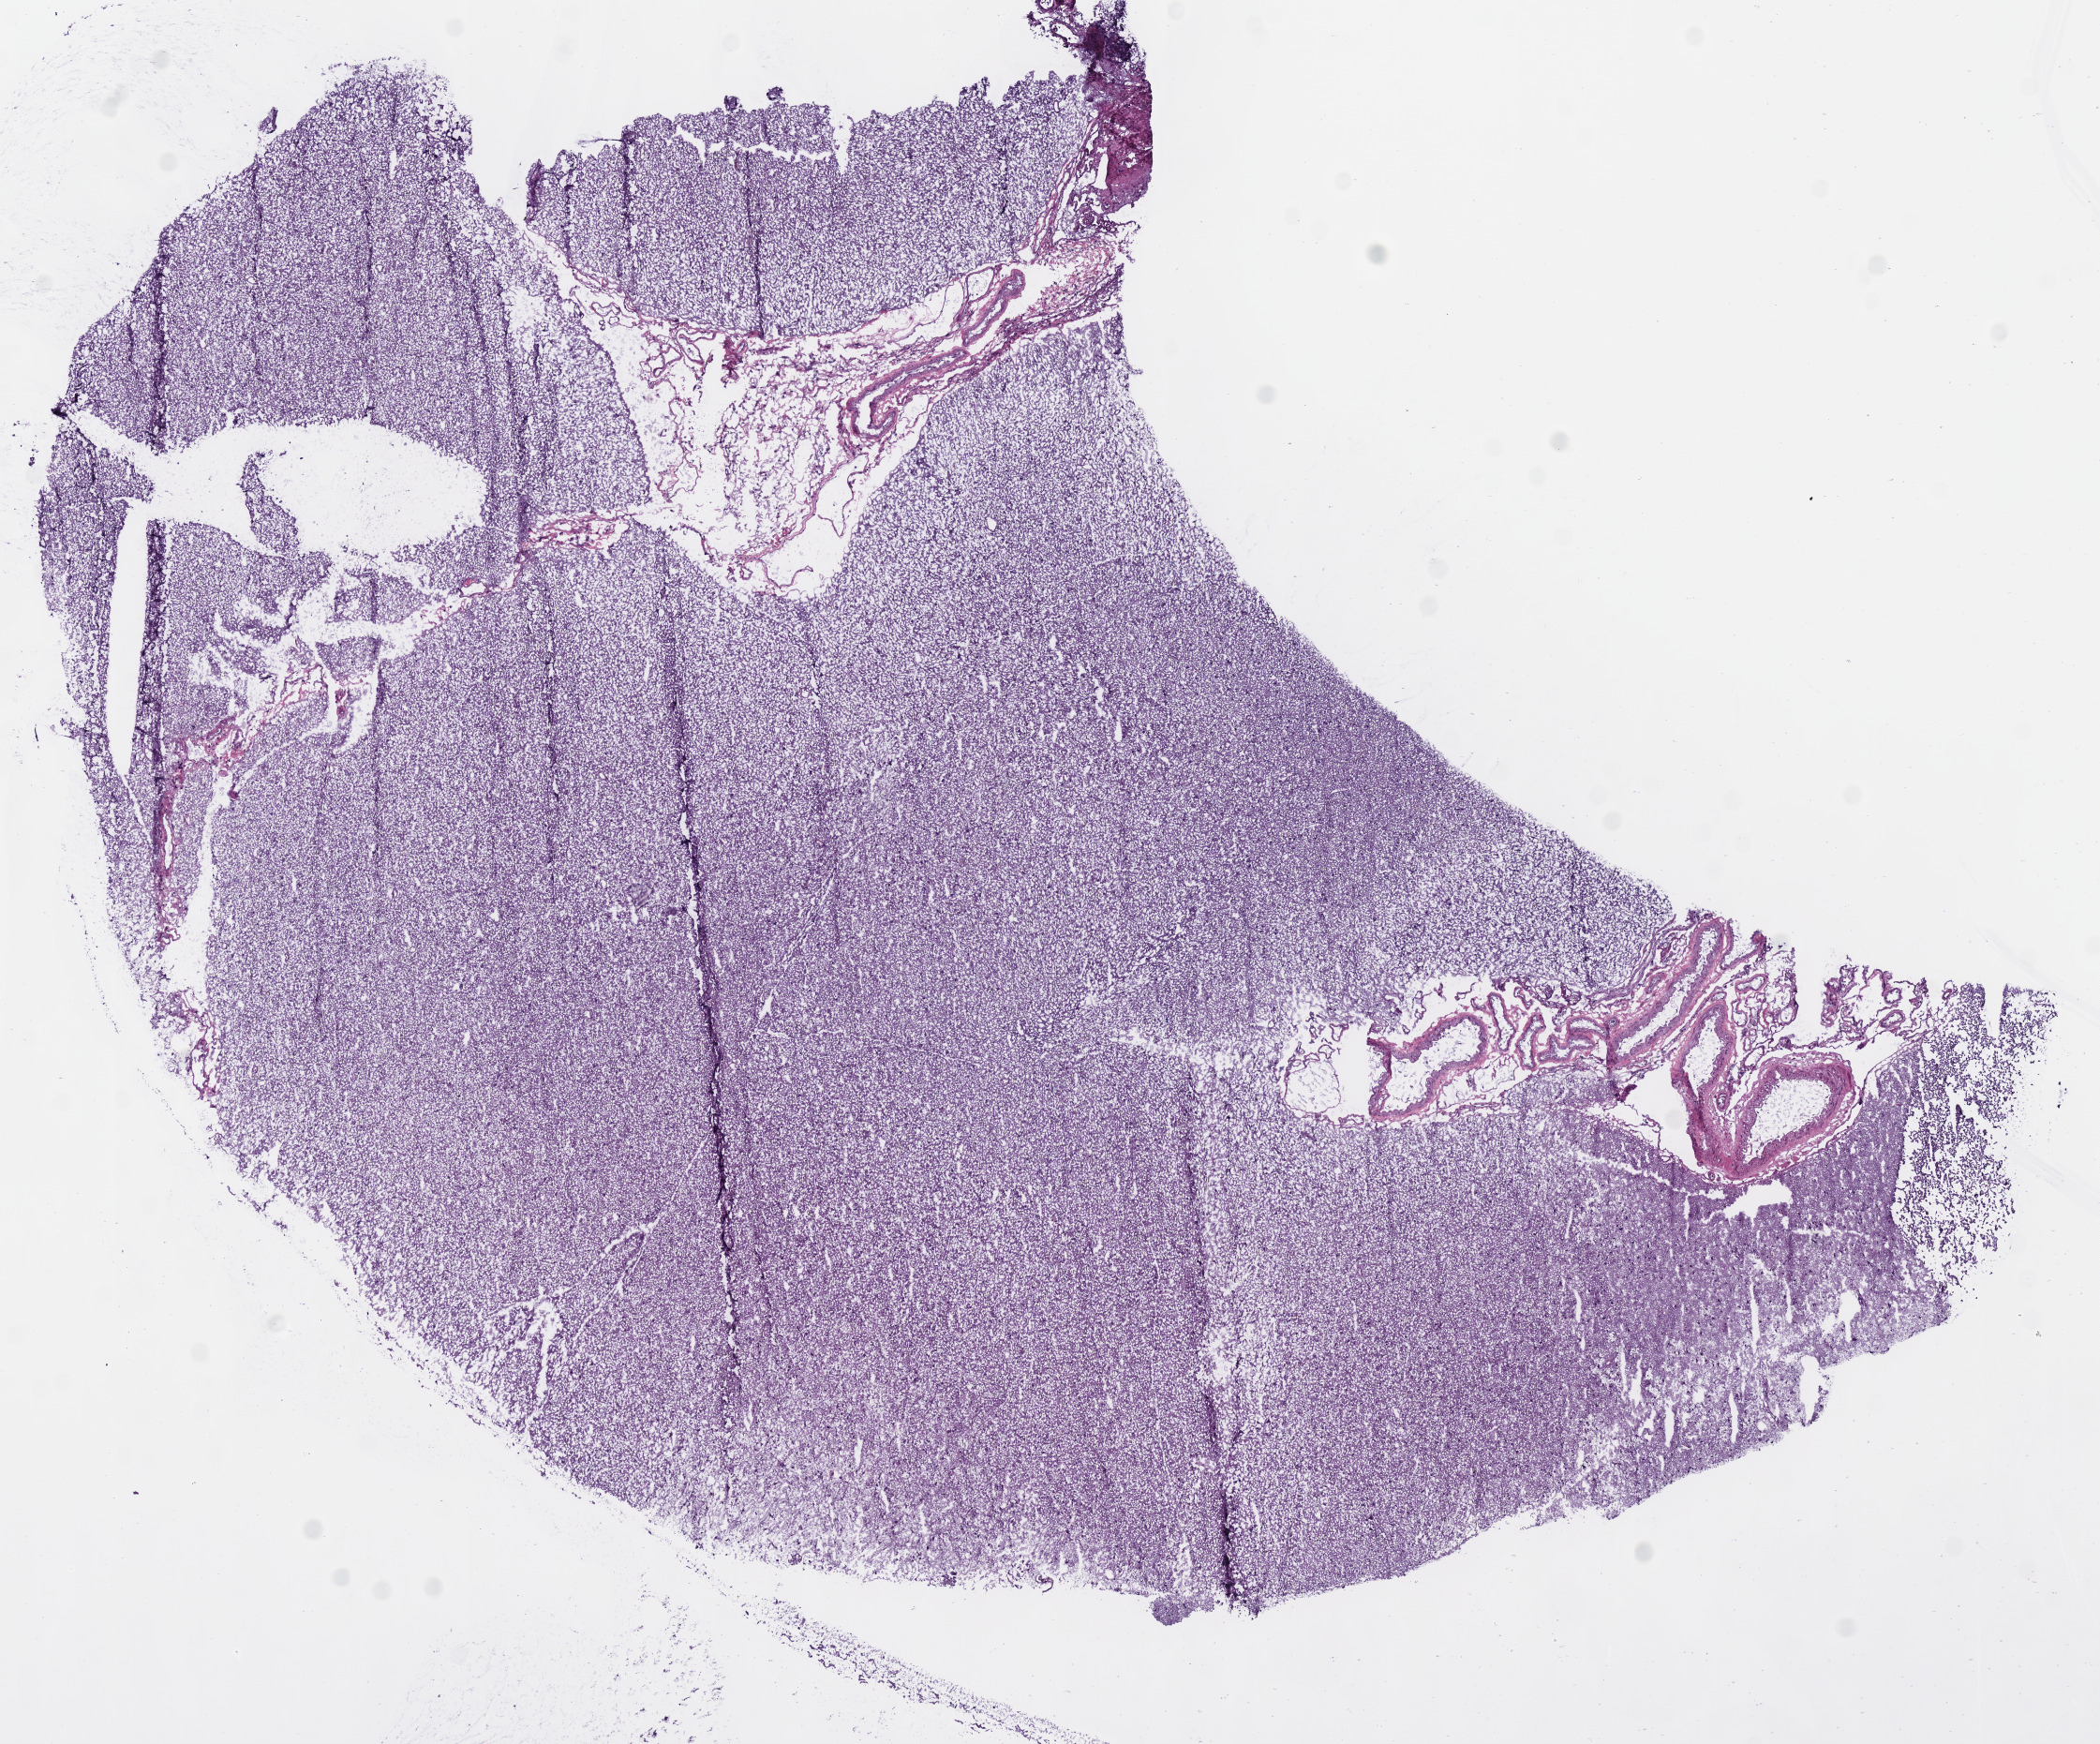
Whole-slide histology image, H&E-stained — low-resolution overview of the scanned area, about 8.8 x 7.3 mm (acquisition: 40x scan), frozen section, sample: primary tumour, brain. Patient: female, age at initial diagnosis 34 years. Histologic grade: G3 (poorly differentiated). Composition of this section per pathologist review: tumour cells 85%, tumour nuclei 60%, normal cells 0%, stromal cells 15%, necrosis 0%.
Histologic diagnosis: Oligodendroglioma, anaplastic (cerebrum).